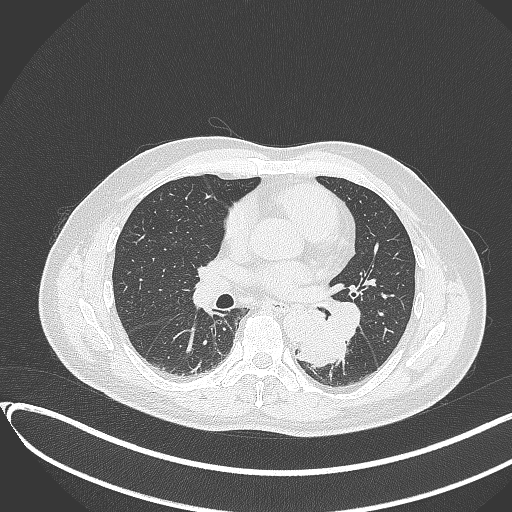
Chest CT, one axial slice. Slice 177 of 417 in the series (ordered by position). Reconstruction kernel B70f. Lung window (W 1500 / L -600 HU). 1 mm slice thickness. 512 × 512 image matrix, field of view 400 × 400 mm. Male patient, age 54 years. Case-level facts recorded for this patient, not image findings: clinical TNM (as recorded): T3 N0 M0.
Annotated regions visible in this slice (bounding box drawn by a radiologist):
- lung tumour (recorded histology: squamous cell carcinoma): bounding box <290,313,348,367> (left, top, right, bottom; pixels)